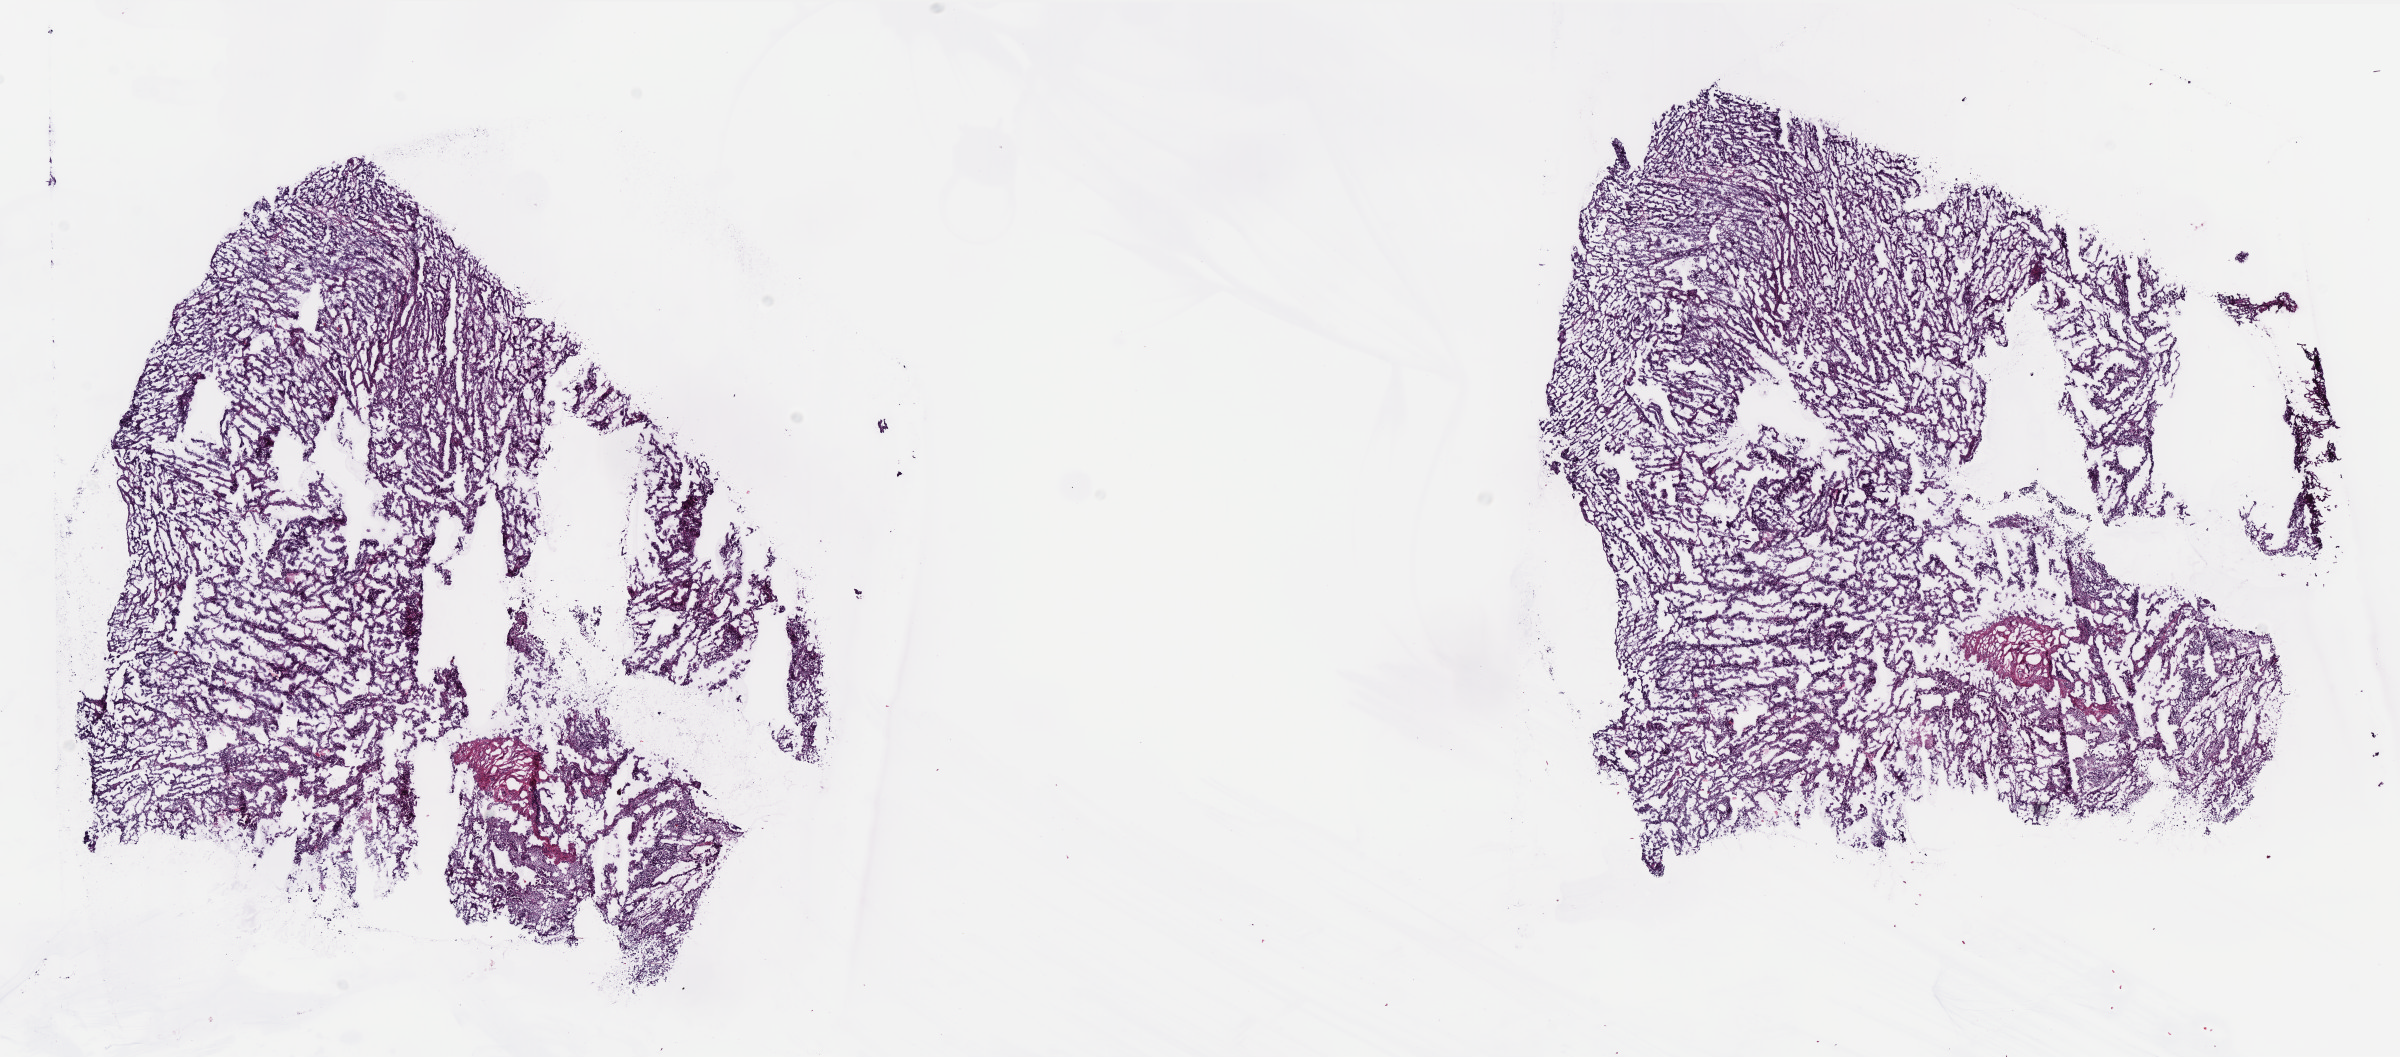
Whole-slide histology image, H&E — whole scanned area (about 19.2 x 8.5 mm, acquisition: 40x scan) shown as a low-resolution overview. Frozen section from the bottom of the tissue portion. Sample: primary tumour, uterus. Female patient; age at initial diagnosis 54 years. Histologic grade: G1 (well differentiated). Pathologist review of this section (percent, as recorded): tumour cells 90%, tumour nuclei 90%, normal cells 0%, stromal cells 10%, necrosis 0%. Inflammatory infiltration, as recorded: lymphocyte infiltration 10%, monocyte infiltration 5%, neutrophil infiltration 10%.
FIGO stage: IA. Histologic diagnosis: Endometrioid adenocarcinoma, NOS.